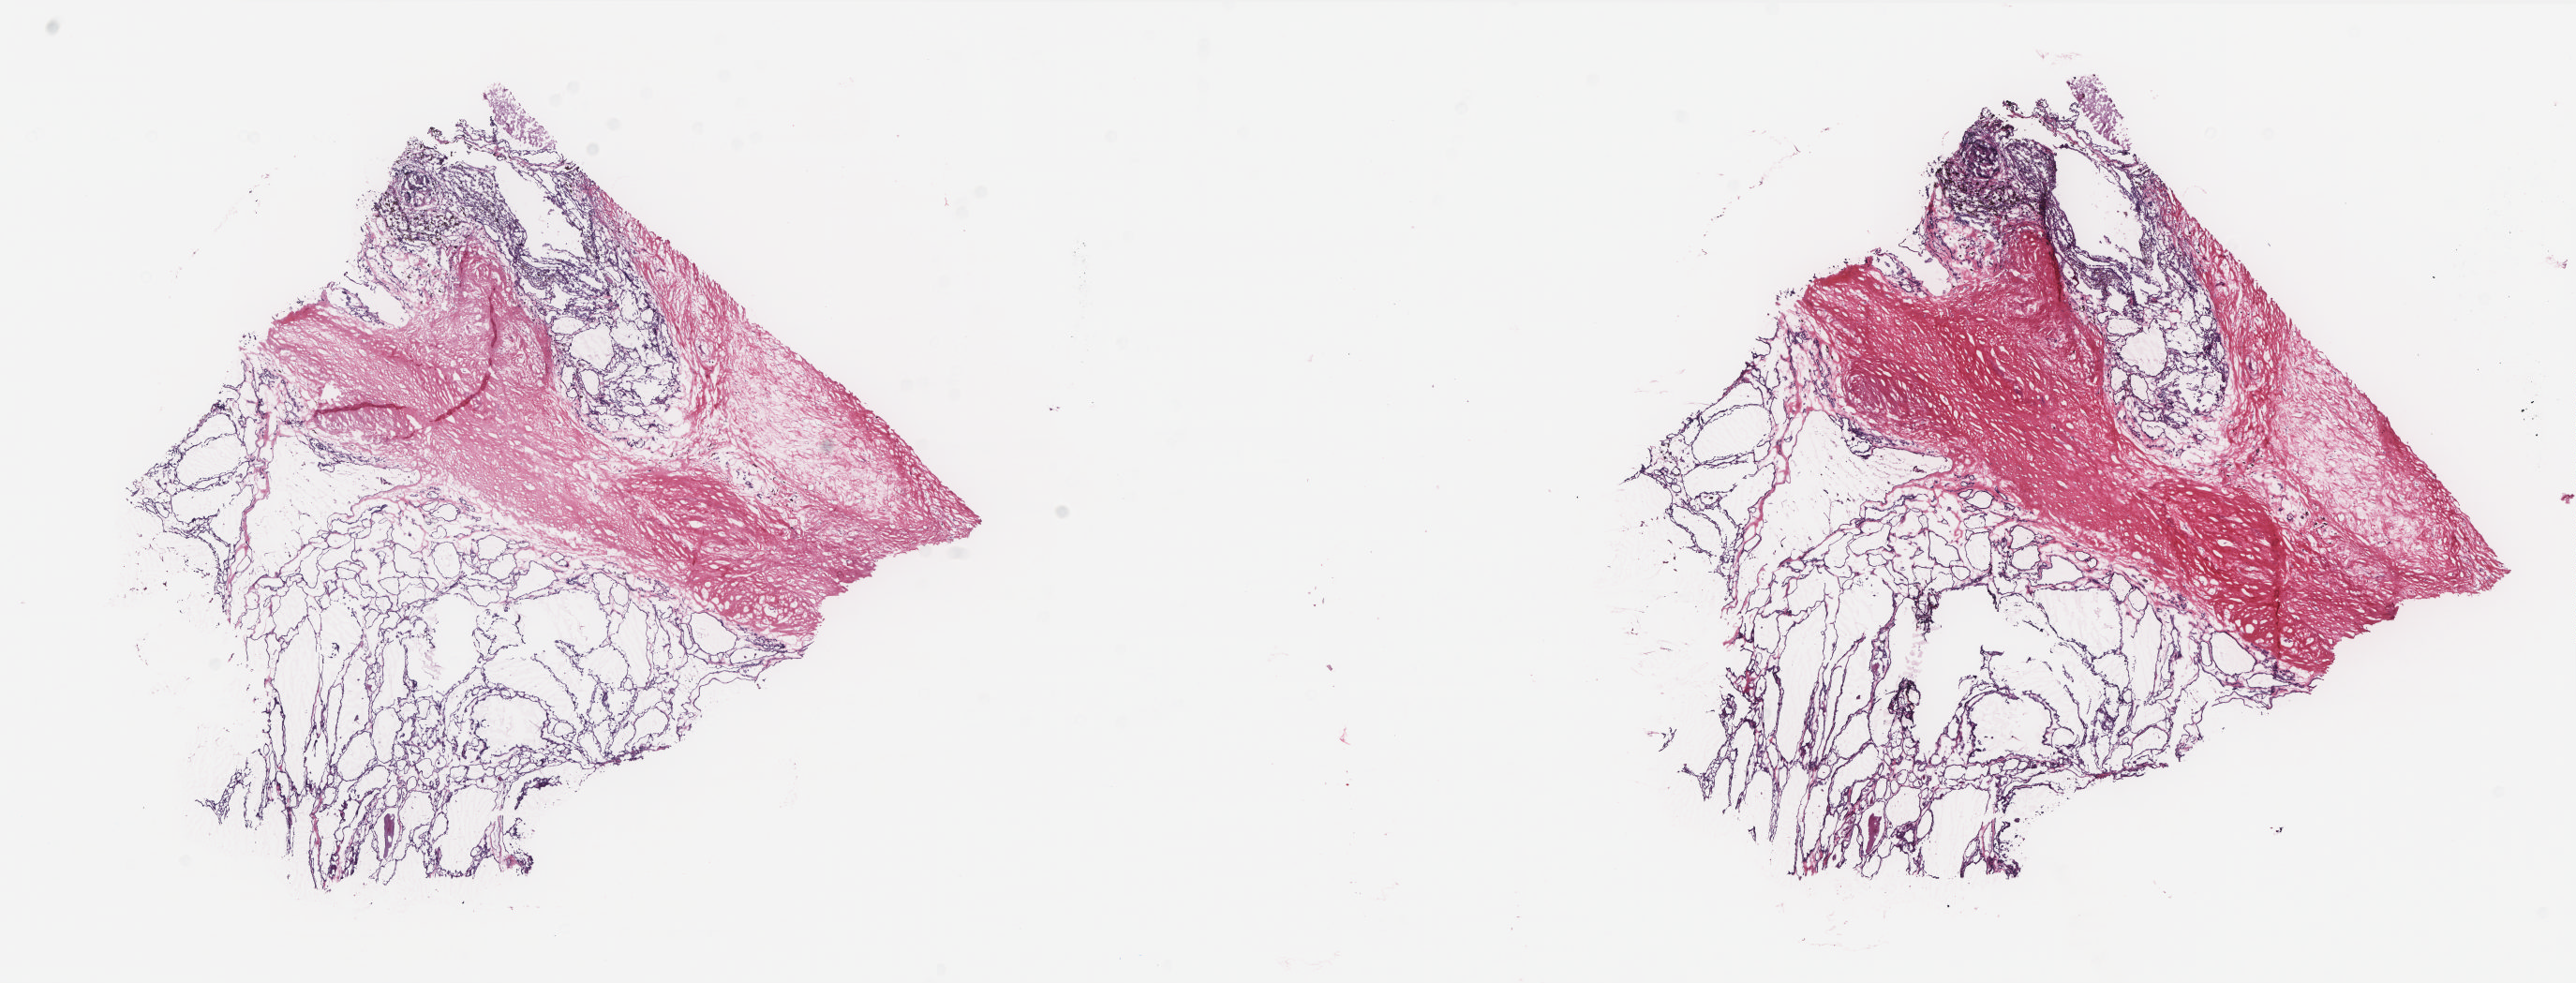
Hematoxylin and eosin (H&E) stained whole-slide image — low-resolution overview of the scanned area, about 22.0 x 8.4 mm. Frozen section. Sample: solid tissue normal (non-tumour tissue), thyroid. Female patient; age at initial diagnosis 72 years. Slide review estimates, as recorded: tumour cells 0%, tumour nuclei 0%, normal cells 70%, stromal cells 30%, necrosis 0%. Inflammatory infiltration, as recorded: lymphocyte infiltration 1%, monocyte infiltration 3%, neutrophil infiltration 0%.
This section: solid tissue normal (non-tumour) sample from the same patient. Patient diagnosis: Papillary adenocarcinoma, NOS (thyroid gland).